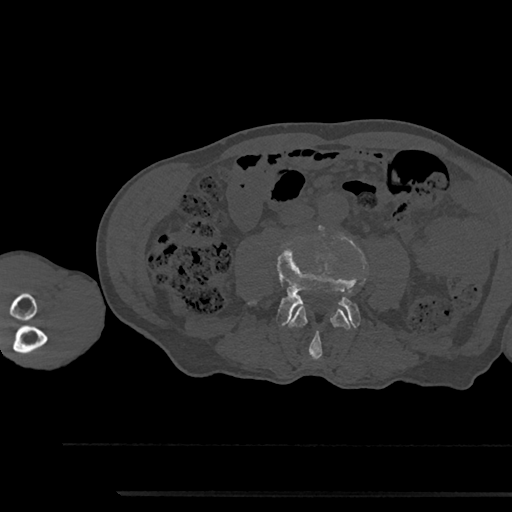
CT including the spine, one axial slice. Bone window (W 1800 / L 400 HU). 512 × 512 image matrix, field of view 367 × 367 mm. Male patient, age 79 years. From the clinical record (not read from this slice): primary cancer: prostate.
Structures marked on this image (semi-automatically segmented with operator editing):
- L3 vertebra: box from (x=288, y=304) to (x=351, y=359) px
- L4 vertebra: (x=253, y=246)–(x=360, y=327)